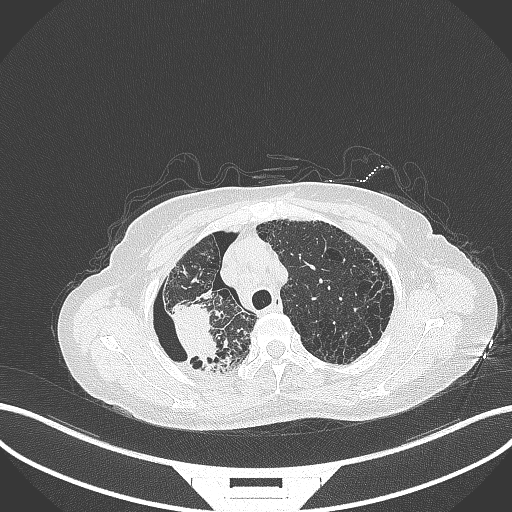
Chest CT, one axial slice. Position 280 of 408 along the scan axis. Reconstruction kernel B70f. 120 kVp. Lung window (W 1500 / L -600 HU). 1 mm slice thickness. 512 × 512 image matrix. Patient: female, 64 years. Case-level facts recorded for this patient, not image findings: clinical TNM (as recorded): T3 N3 M0.
Annotated regions visible in this slice (rectangle marked by the reading radiologist):
- lung tumour (recorded histology: squamous cell carcinoma): bounding box <170,298,225,363> (left, top, right, bottom; pixels)